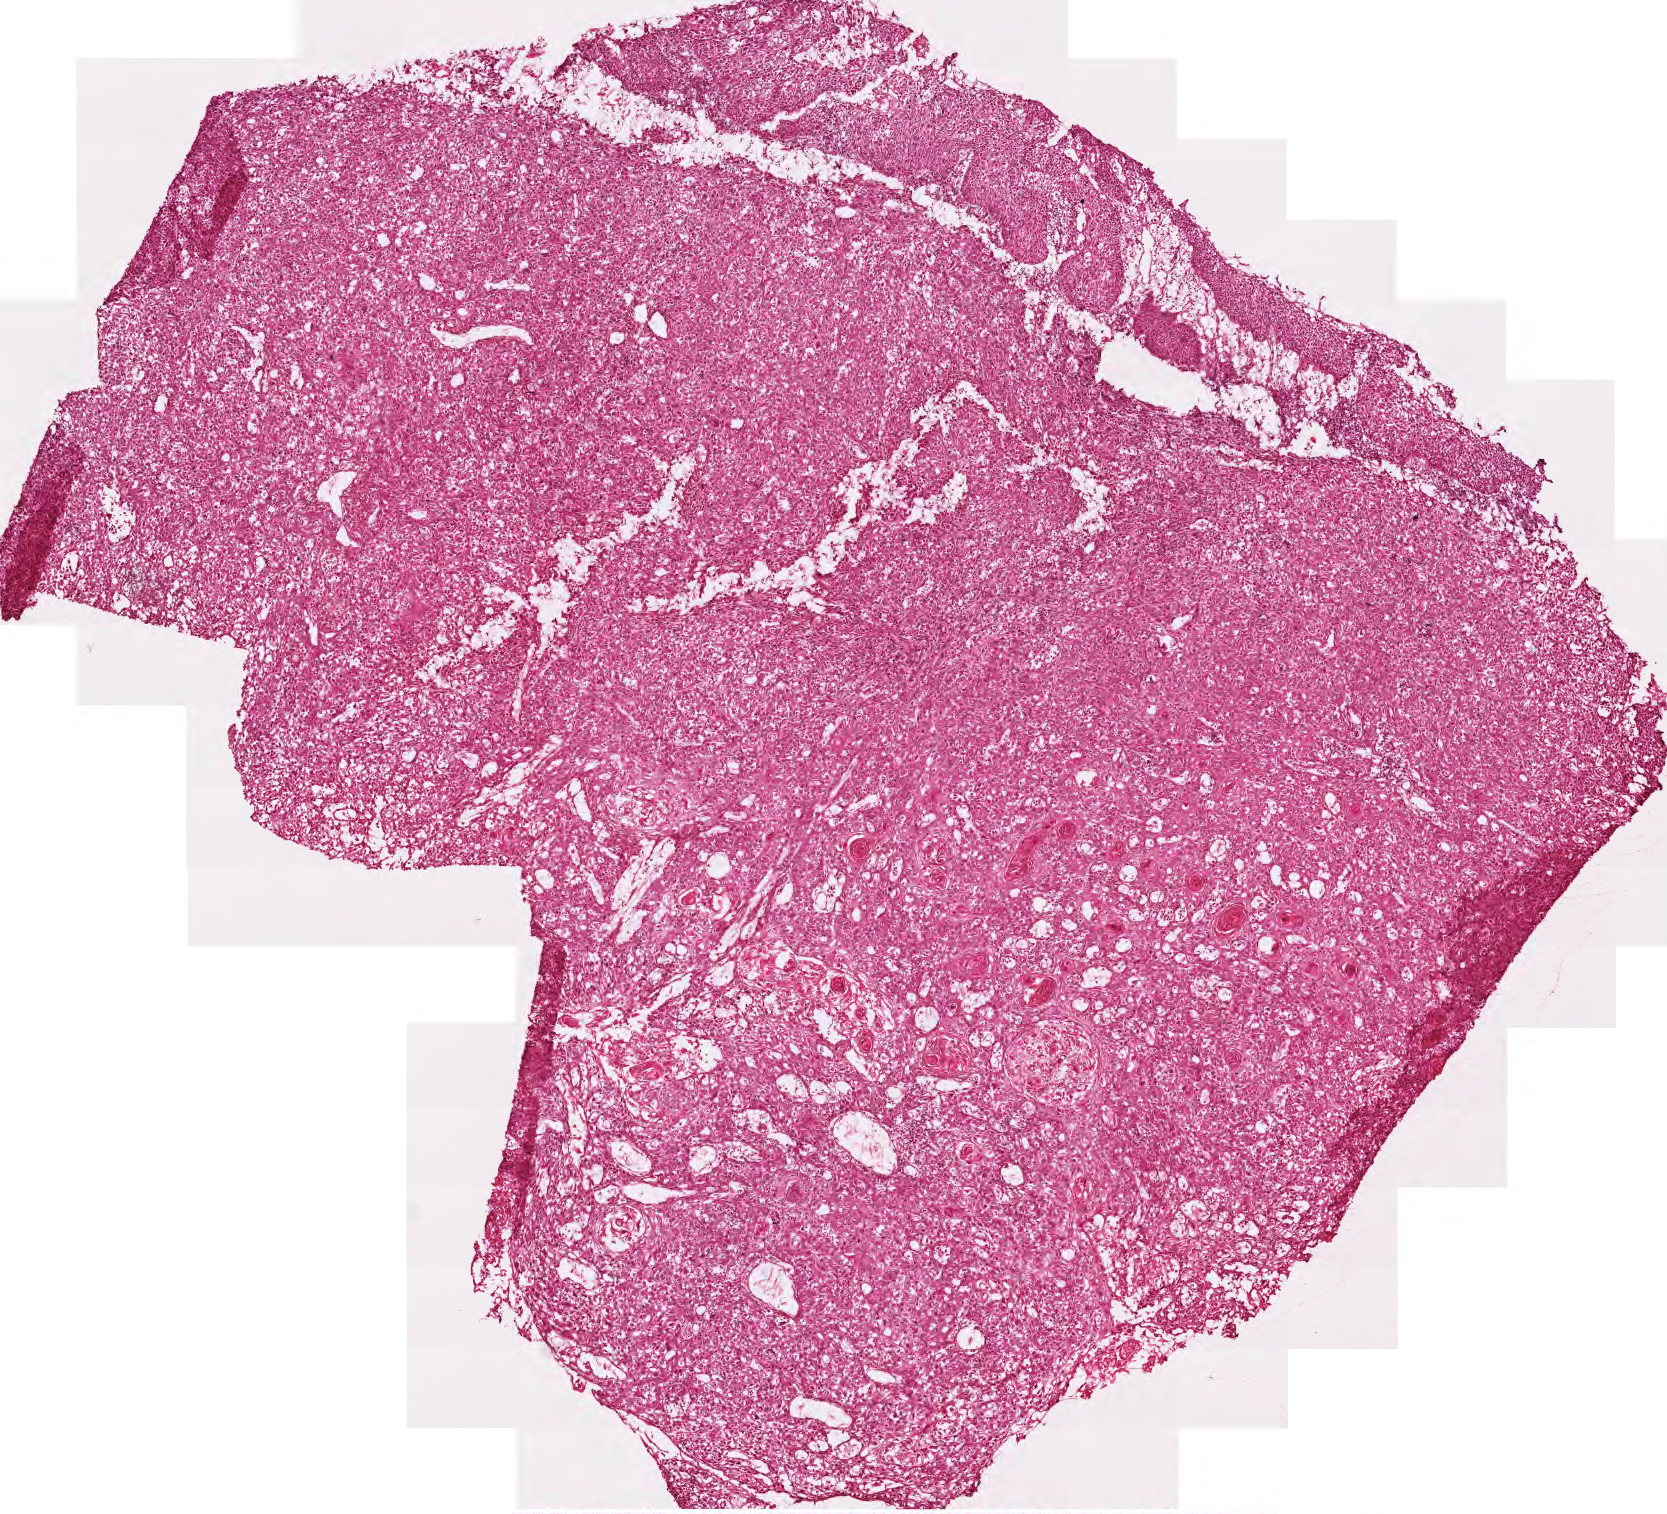
H&E whole-slide image, low-resolution overview of the scanned area, about 3.3 x 3.0 mm; frozen section from the top of the tissue portion; primary tumour sample from the head and neck. Patient: male, age at initial diagnosis 66 years. Histologic grade: G2 (moderately differentiated). Composition of this section per pathologist review: tumour cells 95%, tumour nuclei 70%, normal cells 0%, stromal cells 5%, necrosis 0%.
AJCC pathologic stage: IVA. Laterality: left. Pathologic diagnosis: Squamous cell carcinoma, NOS (overlapping lesion of lip, oral cavity and pharynx).